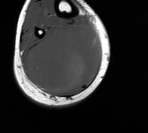
MRI of an extremity soft-tissue mass, one axial slice; position 47 of 76 along the scan axis; MR volume resampled by the dataset authors to the PET/CT grid (not the native acquisition matrix); 3.27 mm slice thickness; 148 × 133 image matrix, field of view 145 × 130 mm. Male patient. Case-level facts recorded for this patient, not image findings: histological type: liposarcoma - round cell; grade: high; site of the primary tumour: right calf.
Outlined on this slice (expert contour drawn on MRI and transferred to this co-registered scan by the dataset authors):
- gross tumour volume (mass): bounding box [x1, y1, x2, y2] px = [24, 23, 101, 93]